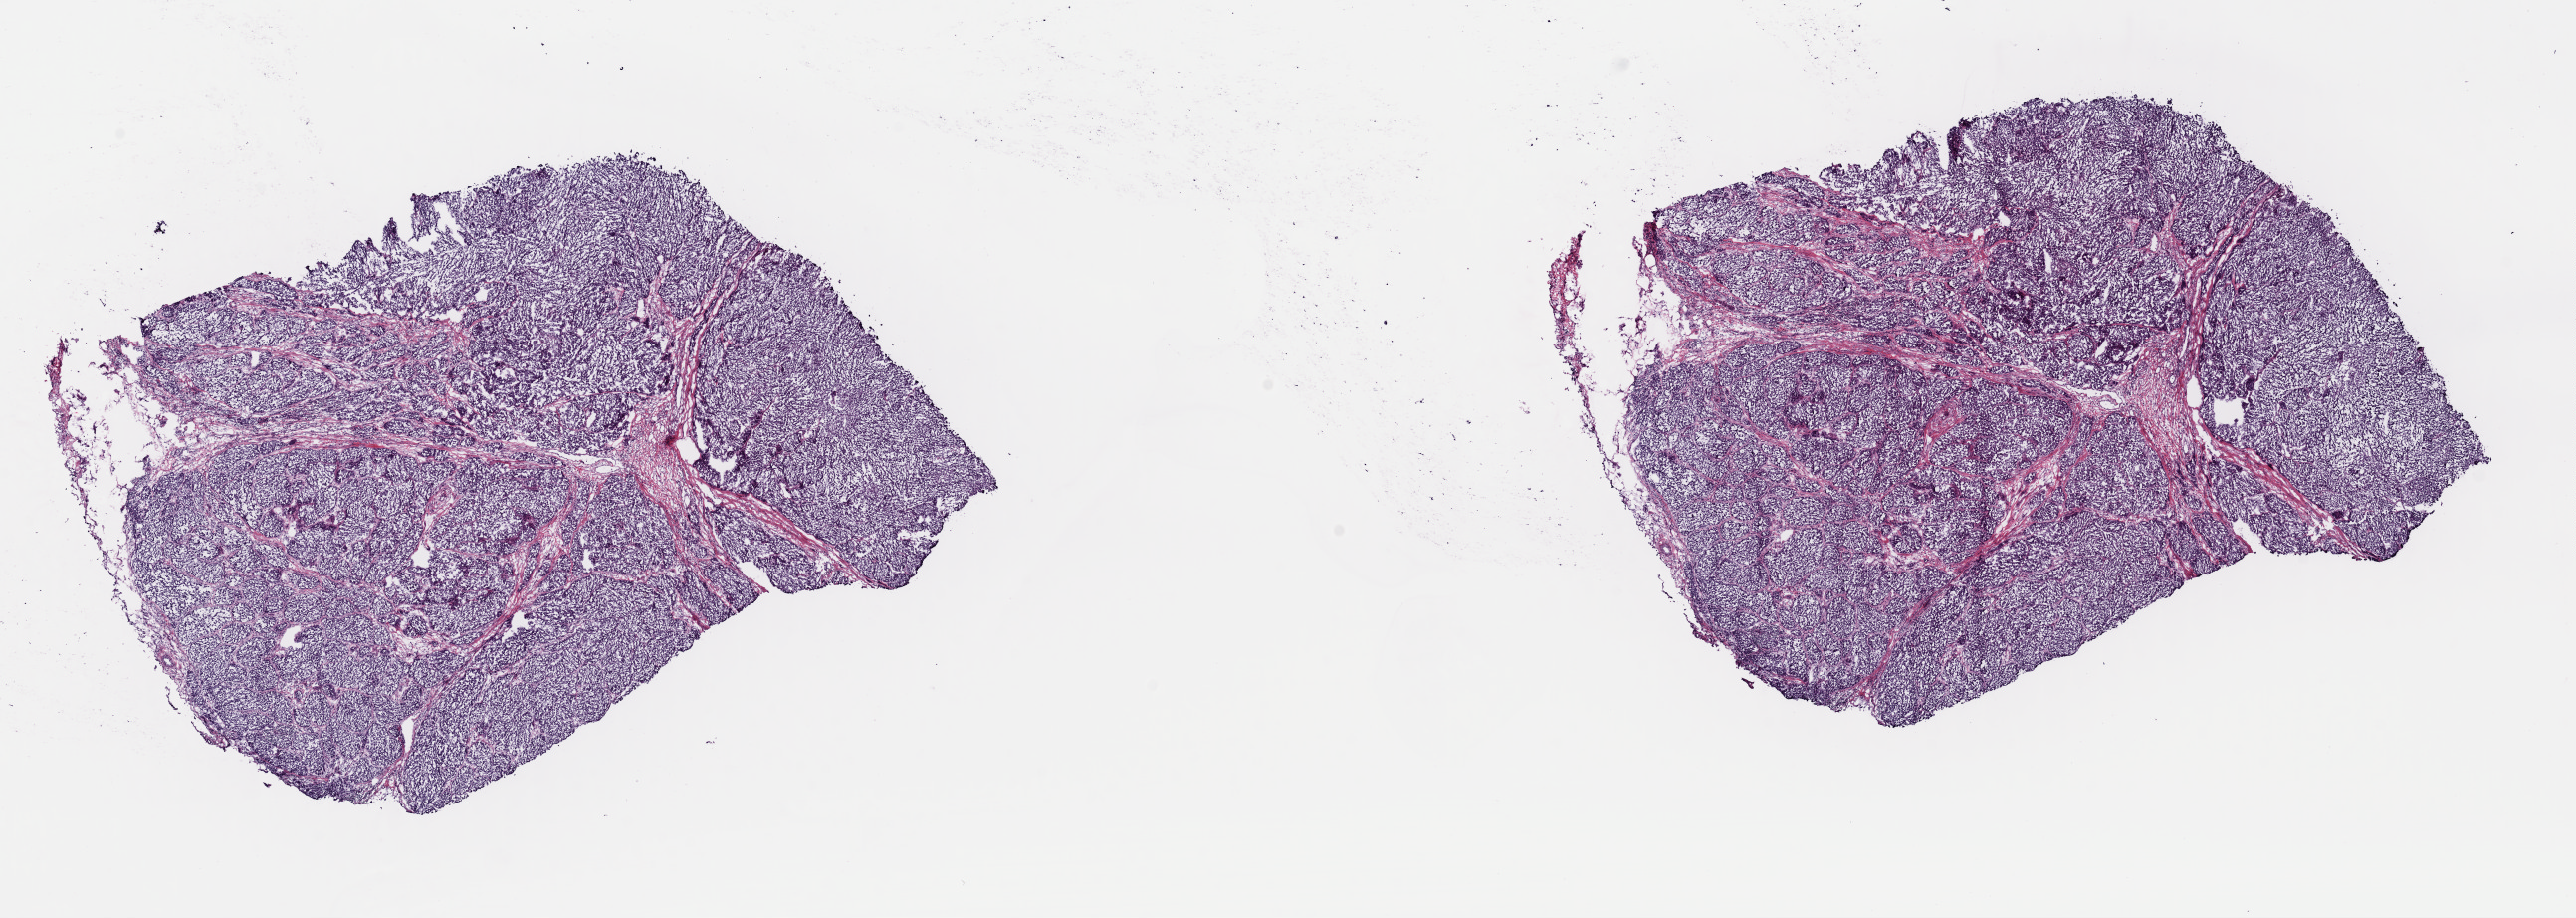
Whole-slide histology image, H&E — whole scanned area (about 20.4 x 7.3 mm) shown as a low-resolution overview. Frozen section. Metastatic tumour sample, sampled site: skin. Female patient; age at initial diagnosis 72 years. Pathologist review of this section (percent, as recorded): tumour cells 100%, tumour nuclei 92%, normal cells 0%, stromal cells 0%, necrosis 0%. Inflammatory infiltration, as recorded: lymphocyte infiltration 0%, monocyte infiltration 0%, neutrophil infiltration 0%.
This section: metastatic tumour tissue. Patient diagnosis: Malignant melanoma, NOS.